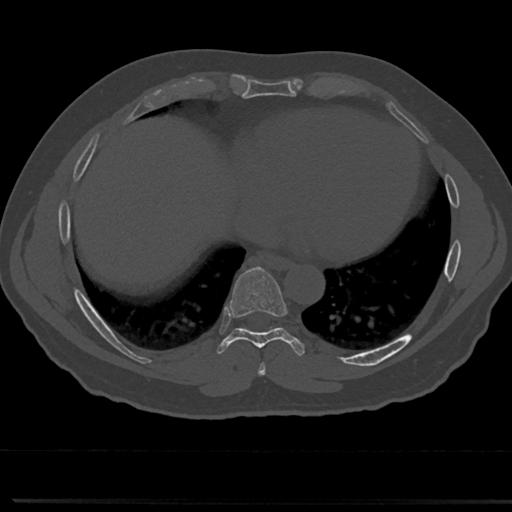
CT including the spine, one axial slice. Slice 351 of 817 in the series (ordered by position). Reconstruction kernel Br40s/3. 120 kVp. Bone window (W 1800 / L 400 HU). 512 × 512 image matrix, field of view 355 × 355 mm. Patient: male, 61 years. From the clinical record (not read from this slice): primary cancer: prostate.
Annotated regions visible in this slice (semi-automatic segmentation, software-assisted and operator-edited):
- T7 vertebra: bounding box (x1, y1, x2, y2) in pixels: (253, 336, 275, 375)
- T8 vertebra: (221, 271, 297, 346)